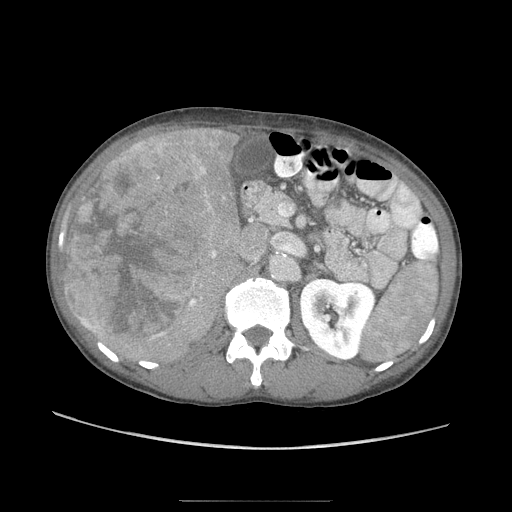
Contrast-enhanced abdominal CT (liver protocol), one axial slice. Position 39 of 103 along the scan axis. Reconstruction kernel STANDARD. Soft-tissue window (W 400 / L 40 HU). 512 × 512 image matrix, field of view 380 × 380 mm. From the clinical record (not read from this slice): diagnosis: hepatocellular carcinoma (patient treated with transarterial chemoembolisation; whether this scan precedes or follows treatment is not stated here); TNM stage (as recorded): Stage-IIIA; Child-Pugh class: A; tumour differentiation: moderately differentiated; tumour nodularity: multinodular.
Structures marked on this image (semi-automatically segmented with operator editing):
- liver parenchyma outside the tumour (the mass and vessels are separate outlines, so this box may not span the whole liver): box from (x=63, y=126) to (x=250, y=361) px
- mass: (x=64, y=136)–(x=220, y=346)
- liver vessels: (x=85, y=302)–(x=191, y=325)